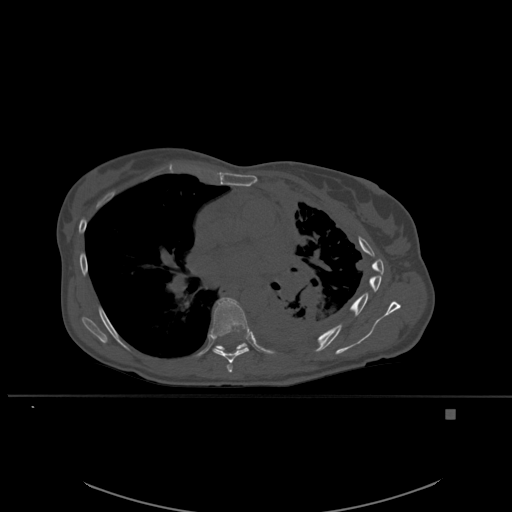
CT including the spine, one axial slice; slice 363 of 537 in the series (ordered by position); bone window (W 1800 / L 400 HU); 1.5 mm slice thickness; 512 × 512 image matrix, field of view 440 × 440 mm. Female patient, age 45 years. From the clinical record (not read from this slice): primary cancer: lung.
Structures marked on this image (semi-automatic segmentation, software-assisted and operator-edited):
- T6 vertebra: bounding box [x1, y1, x2, y2] px = [226, 362, 233, 373]
- T7 vertebra: [210, 297, 249, 363]
- T8 vertebra: [214, 342, 248, 353]